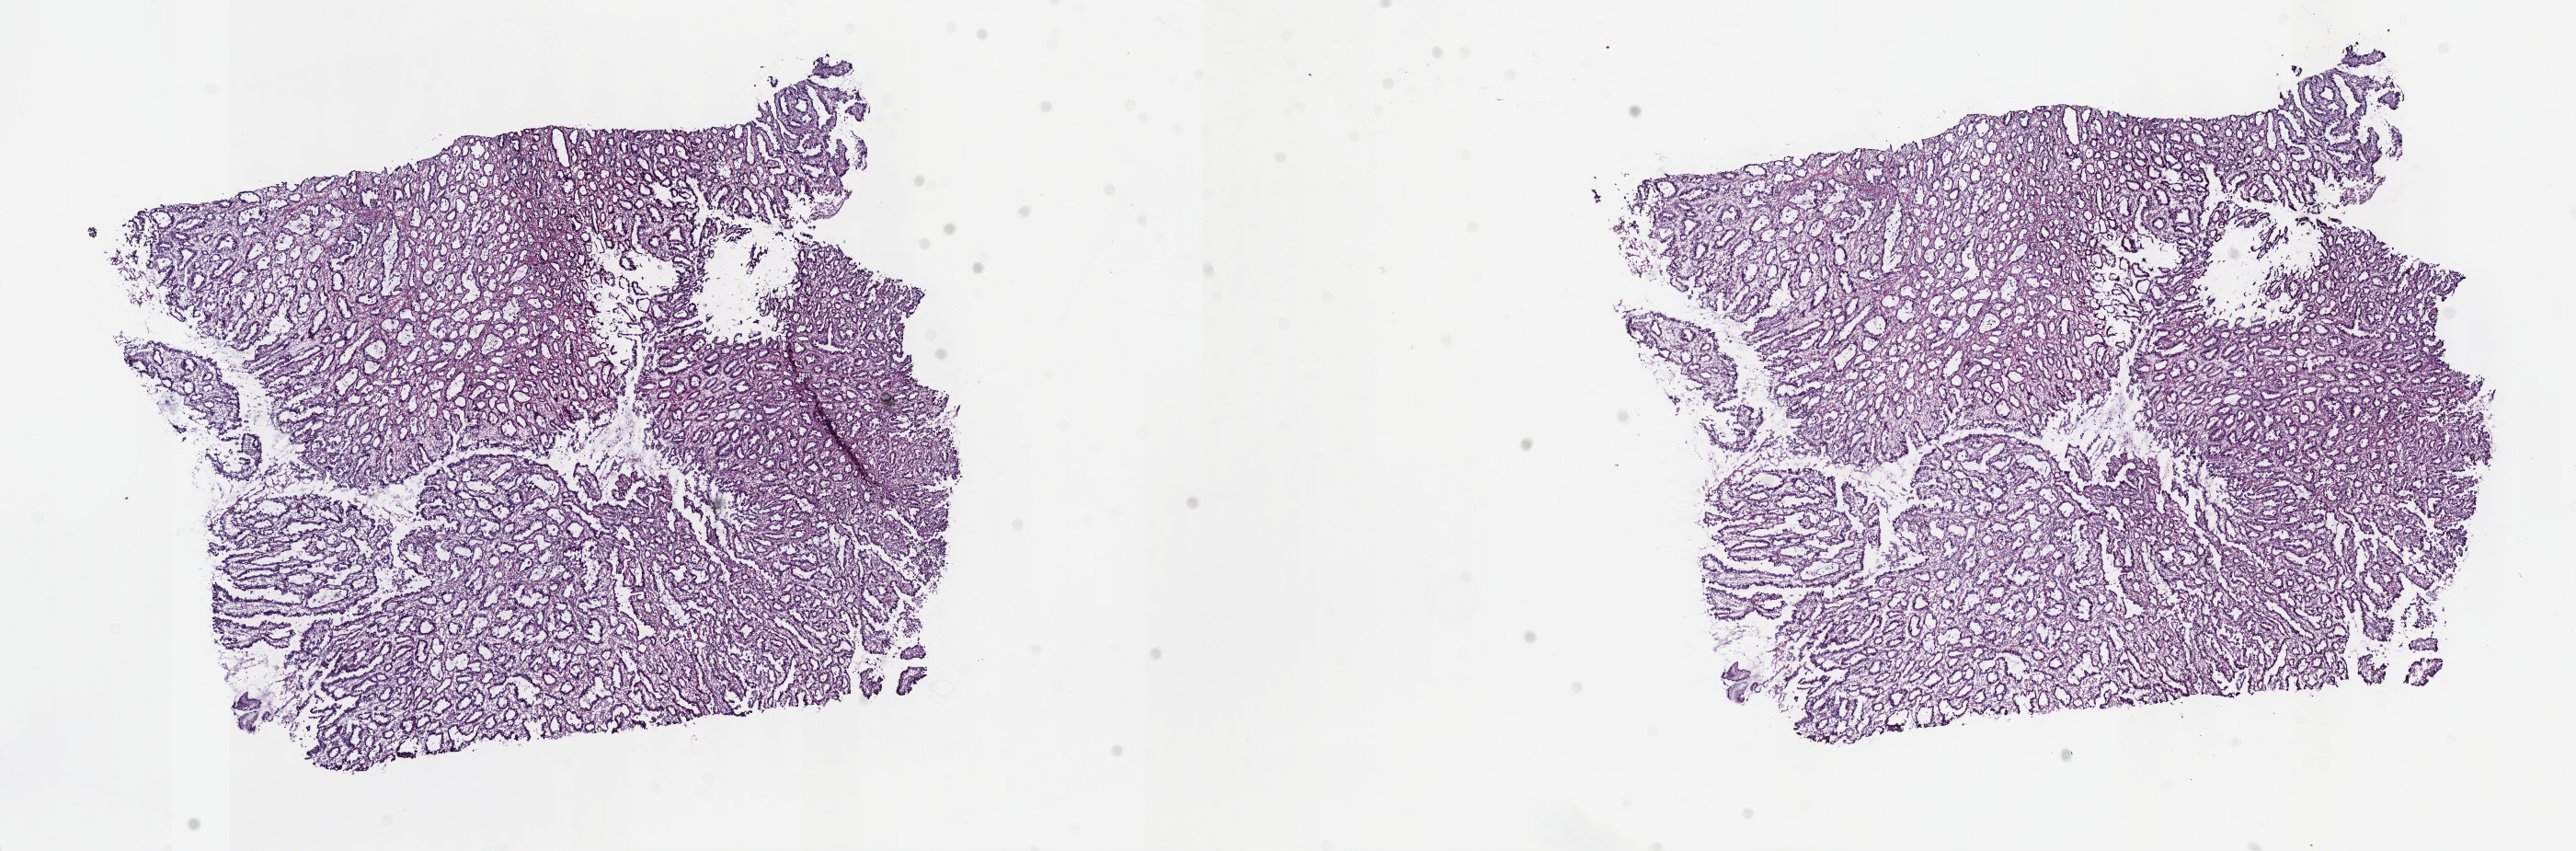
Hematoxylin and eosin (H&E) stained whole-slide image, low-resolution overview of the scanned area, about 22.7 x 7.5 mm, frozen section from the top of the tissue portion, primary tumour sample from the stomach. Male, age 66 years at initial diagnosis. Histologic grade: G2 (moderately differentiated). Slide review estimates, as recorded: tumour cells 50%, tumour nuclei 60%, normal cells 0%, stromal cells 50%, necrosis 0%. Inflammatory infiltration, as recorded: lymphocyte infiltration 0%, monocyte infiltration 0%, neutrophil infiltration 0%.
AJCC pathologic stage: IIIA (7th edition). Diagnosis: Tubular adenocarcinoma (gastric antrum). Lymph nodes positive (case pathology): 6 of 6 examined.